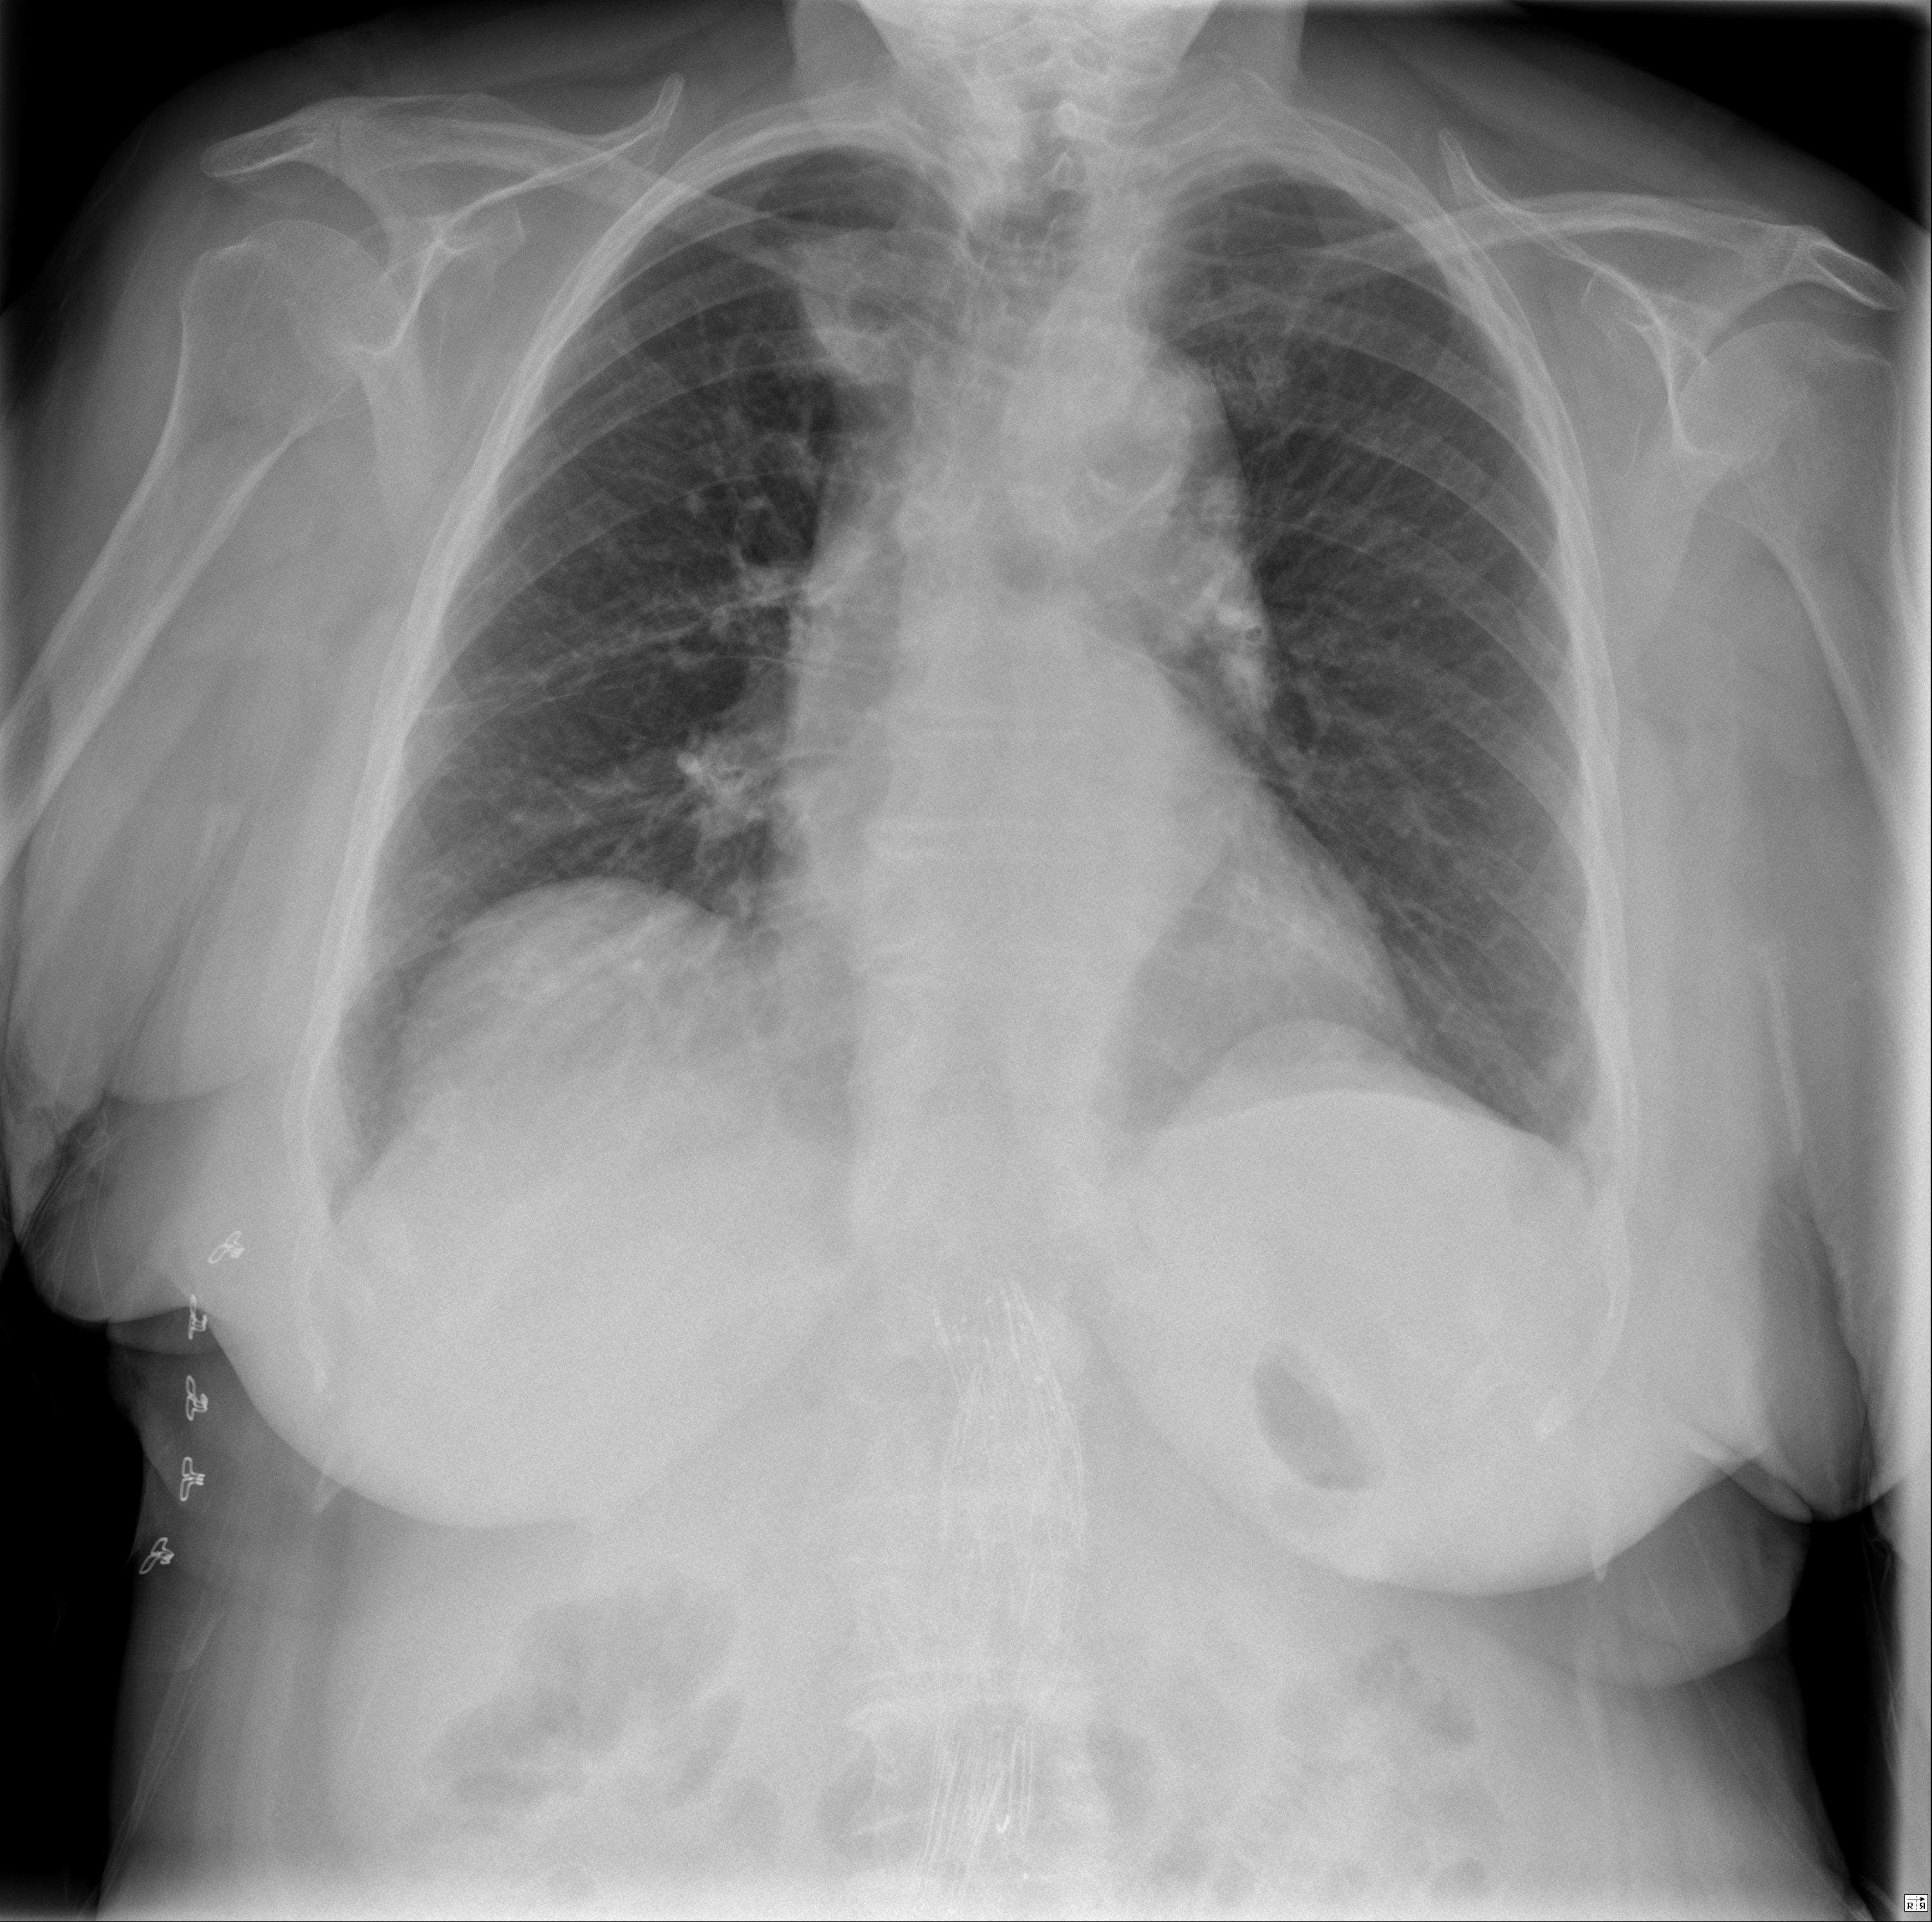
Chest X-ray, PA projection. Female patient, age 88 years; imaged 0 days after the COVID-19 diagnosis.
Radiologist's key findings for this exam: No pleural effusions.